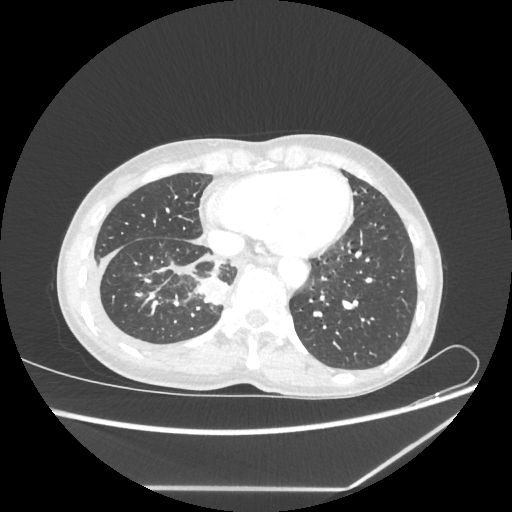
Chest CT, one axial slice; position 65 of 237 along the scan axis; reconstruction kernel STANDARD; 80 kVp; lung window (W 1500 / L -600 HU); 1.25 mm slice thickness; 512 × 512 image matrix, field of view 364 × 364 mm. Female patient, age 59 years. From the clinical record (not read from this slice): clinical TNM (as recorded): T1c N1 M1.
Annotated regions visible in this slice (bounding box drawn by a radiologist):
- lung tumour (recorded histology: adenocarcinoma): bounding box <198,274,226,308> (left, top, right, bottom; pixels)